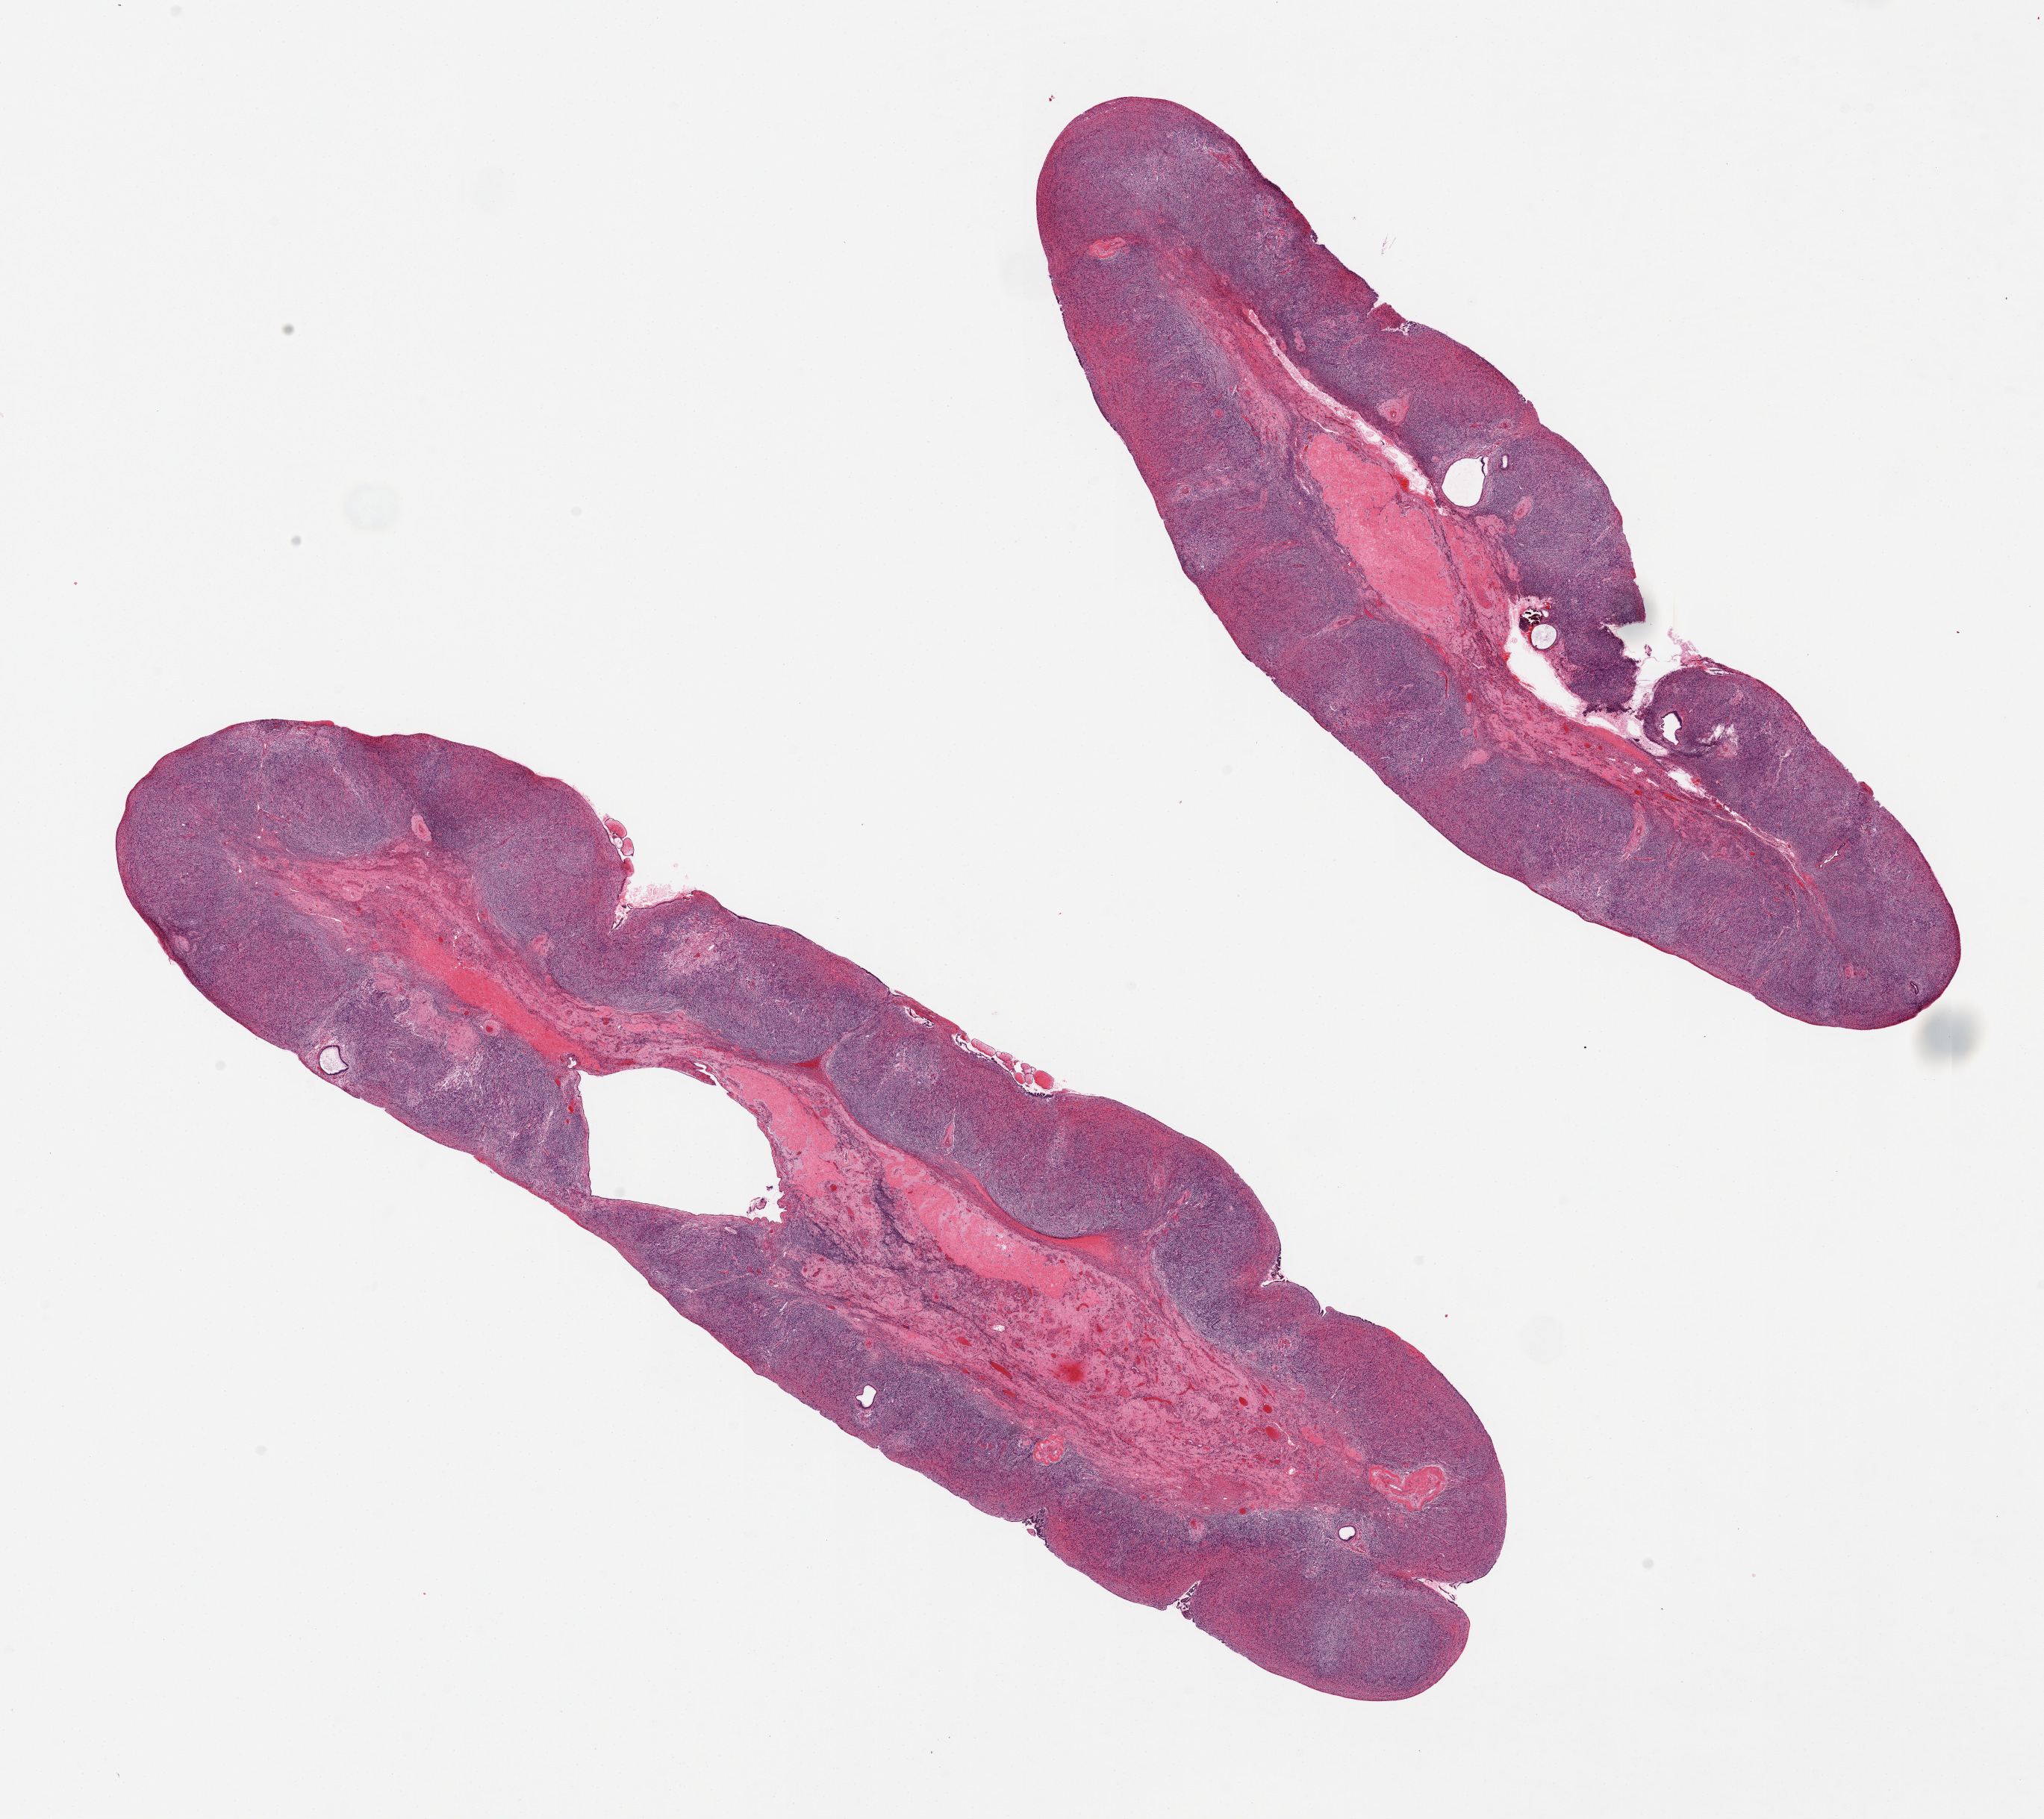
Whole-slide image, haematoxylin and eosin stain — whole scanned area (about 21.7 x 19.3 mm, acquisition: 20x scan) shown as a low-resolution overview. PAXgene-fixed paraffin-embedded (PFPE) section. Section of ovary (target tissue). Donor tissue sample. Female donor.
- reviewer comment on this tissue sample: 2 pieces; atrophic, corpora albicans, several small cysts